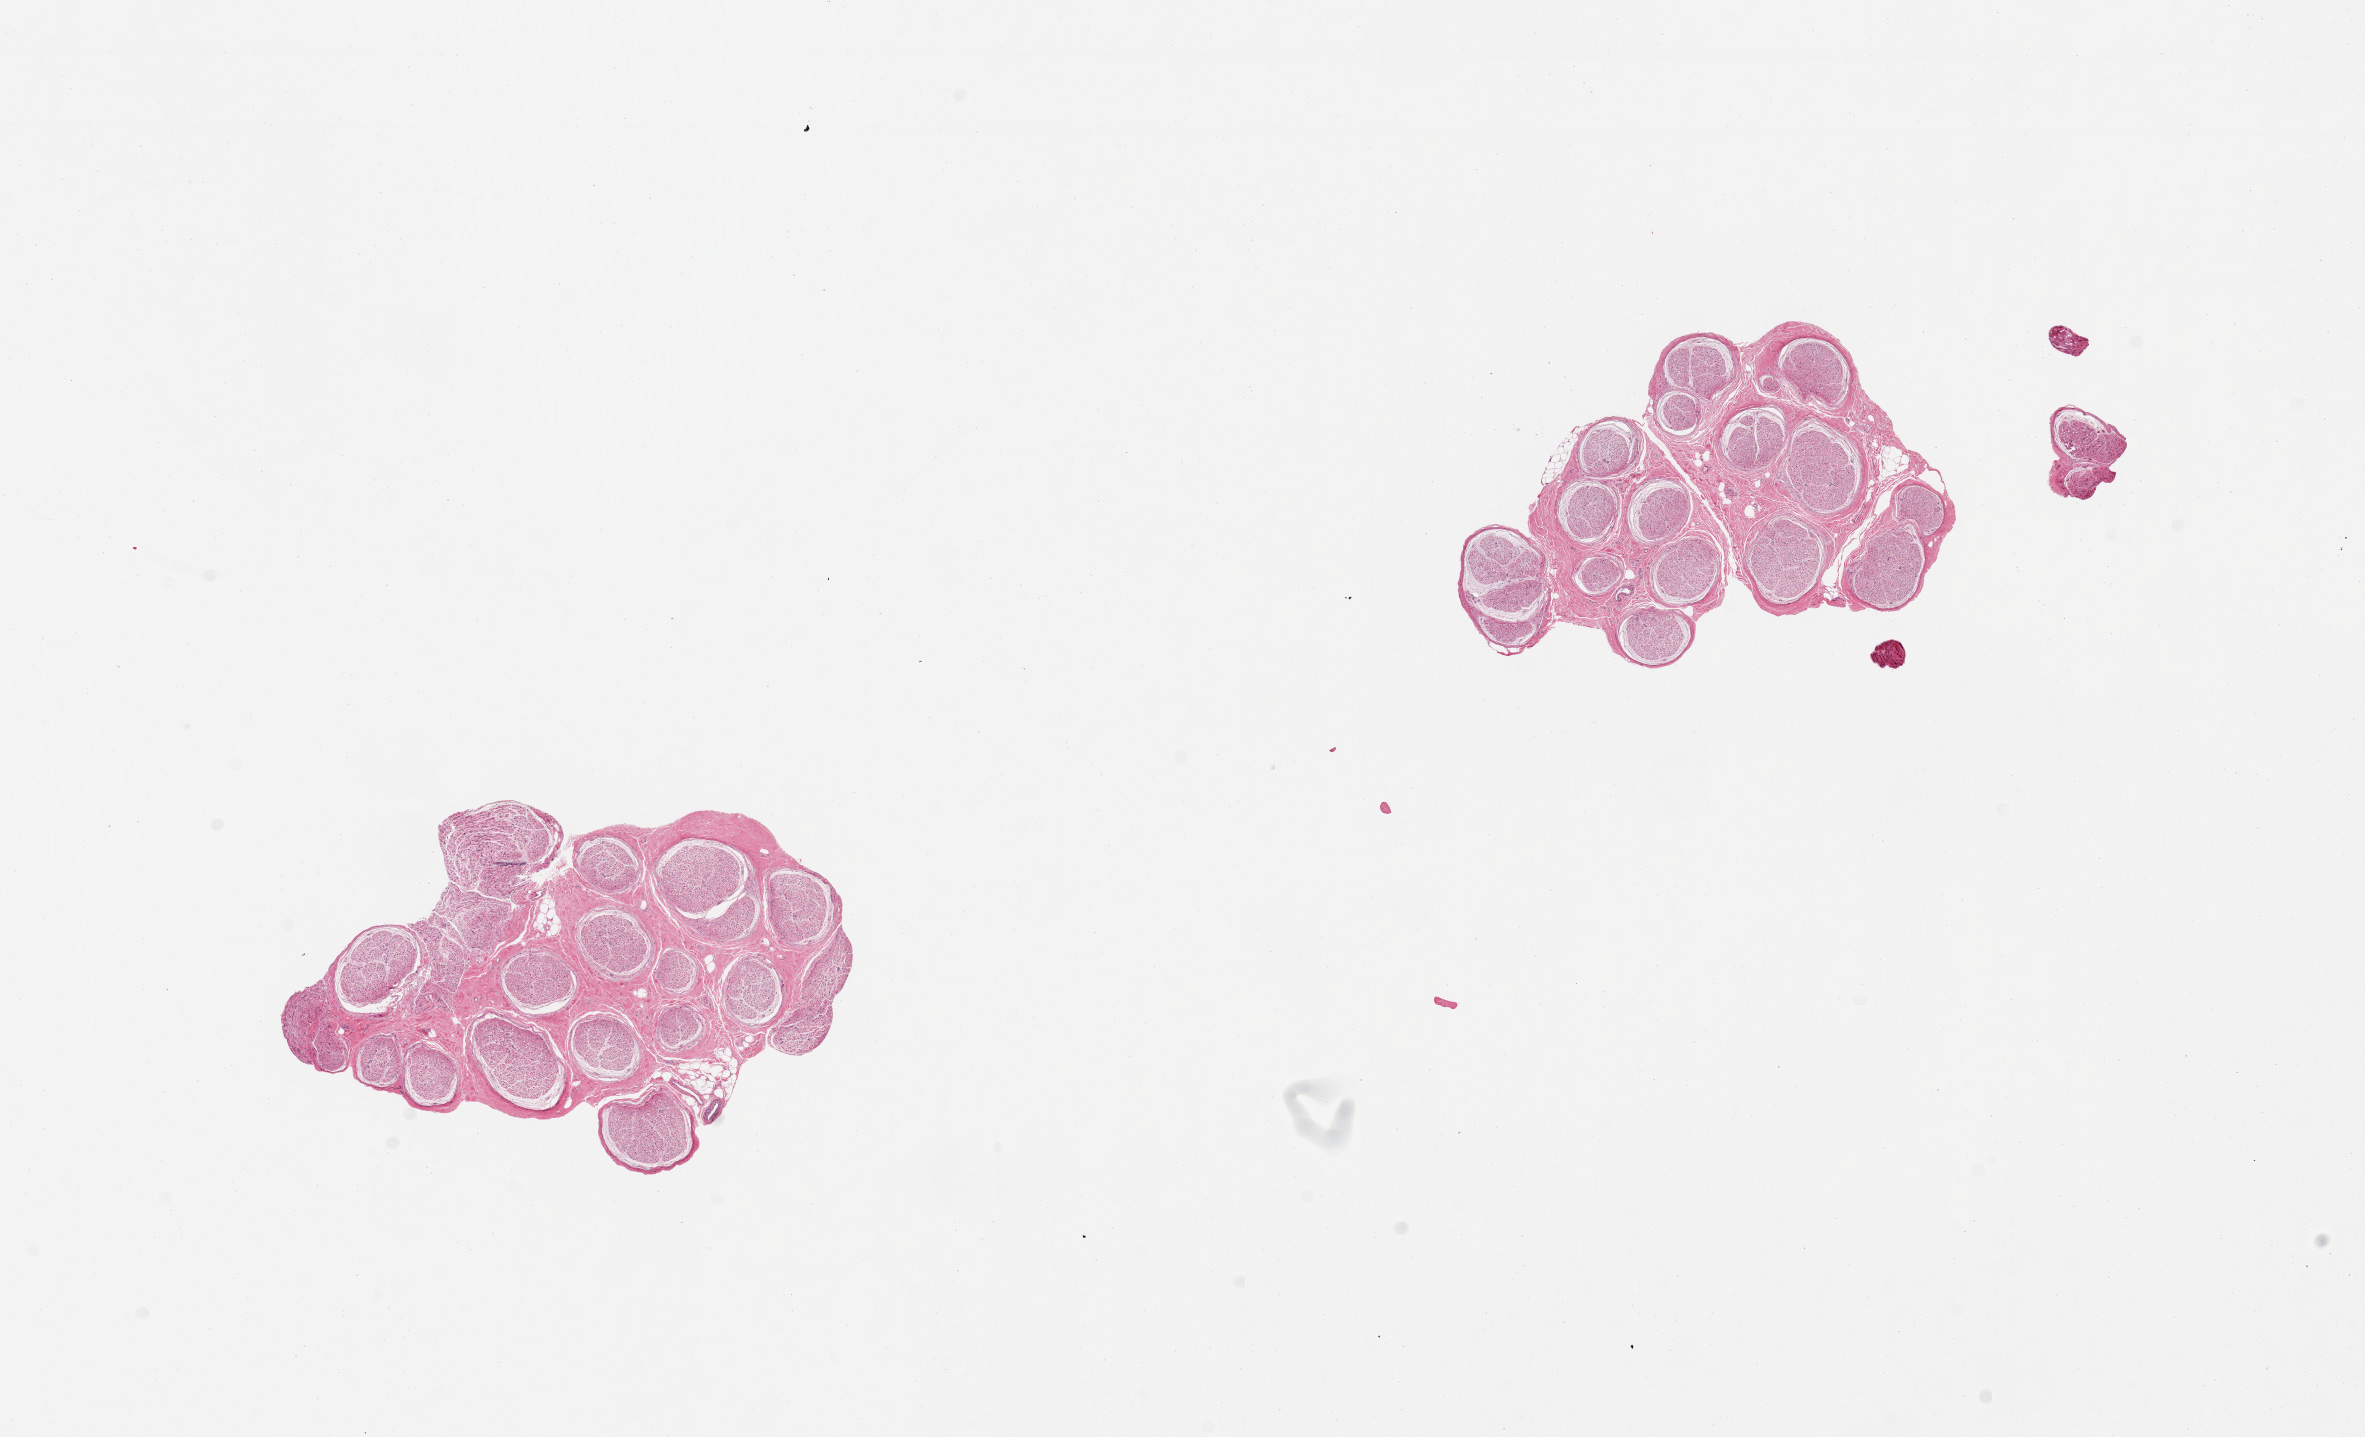
Hematoxylin and eosin (H&E) whole-slide image, low-resolution overview of the scanned area, about 18.7 x 11.4 mm (slide scanned at 20x). PAXgene-fixed paraffin-embedded (PFPE) section. Sampled site (target tissue): tibial nerve. Donor tissue sample.
Reviewer comment on this tissue sample: 2 pieces, 4.5x3 & 4x3mm; good clean specimens.